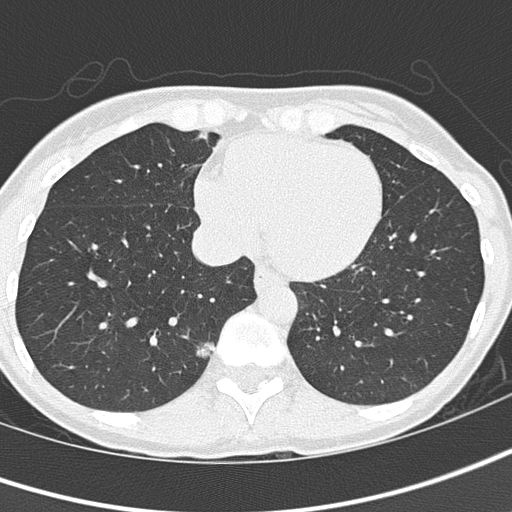
Low-dose screening chest CT, one axial slice. Slice 46 of 145 in the series (ordered by position). Reconstruction kernel B50f. 120 kVp. Lung window (W 1500 / L -600 HU). 2 mm slice thickness. 512 × 512 image matrix, field of view 276 × 276 mm.
Annotated regions visible in this slice (outlined manually by an expert reader):
- lesion 1 (tumor, lower lobe of right lung): bounding box [x1, y1, x2, y2] px = [197, 343, 215, 357]